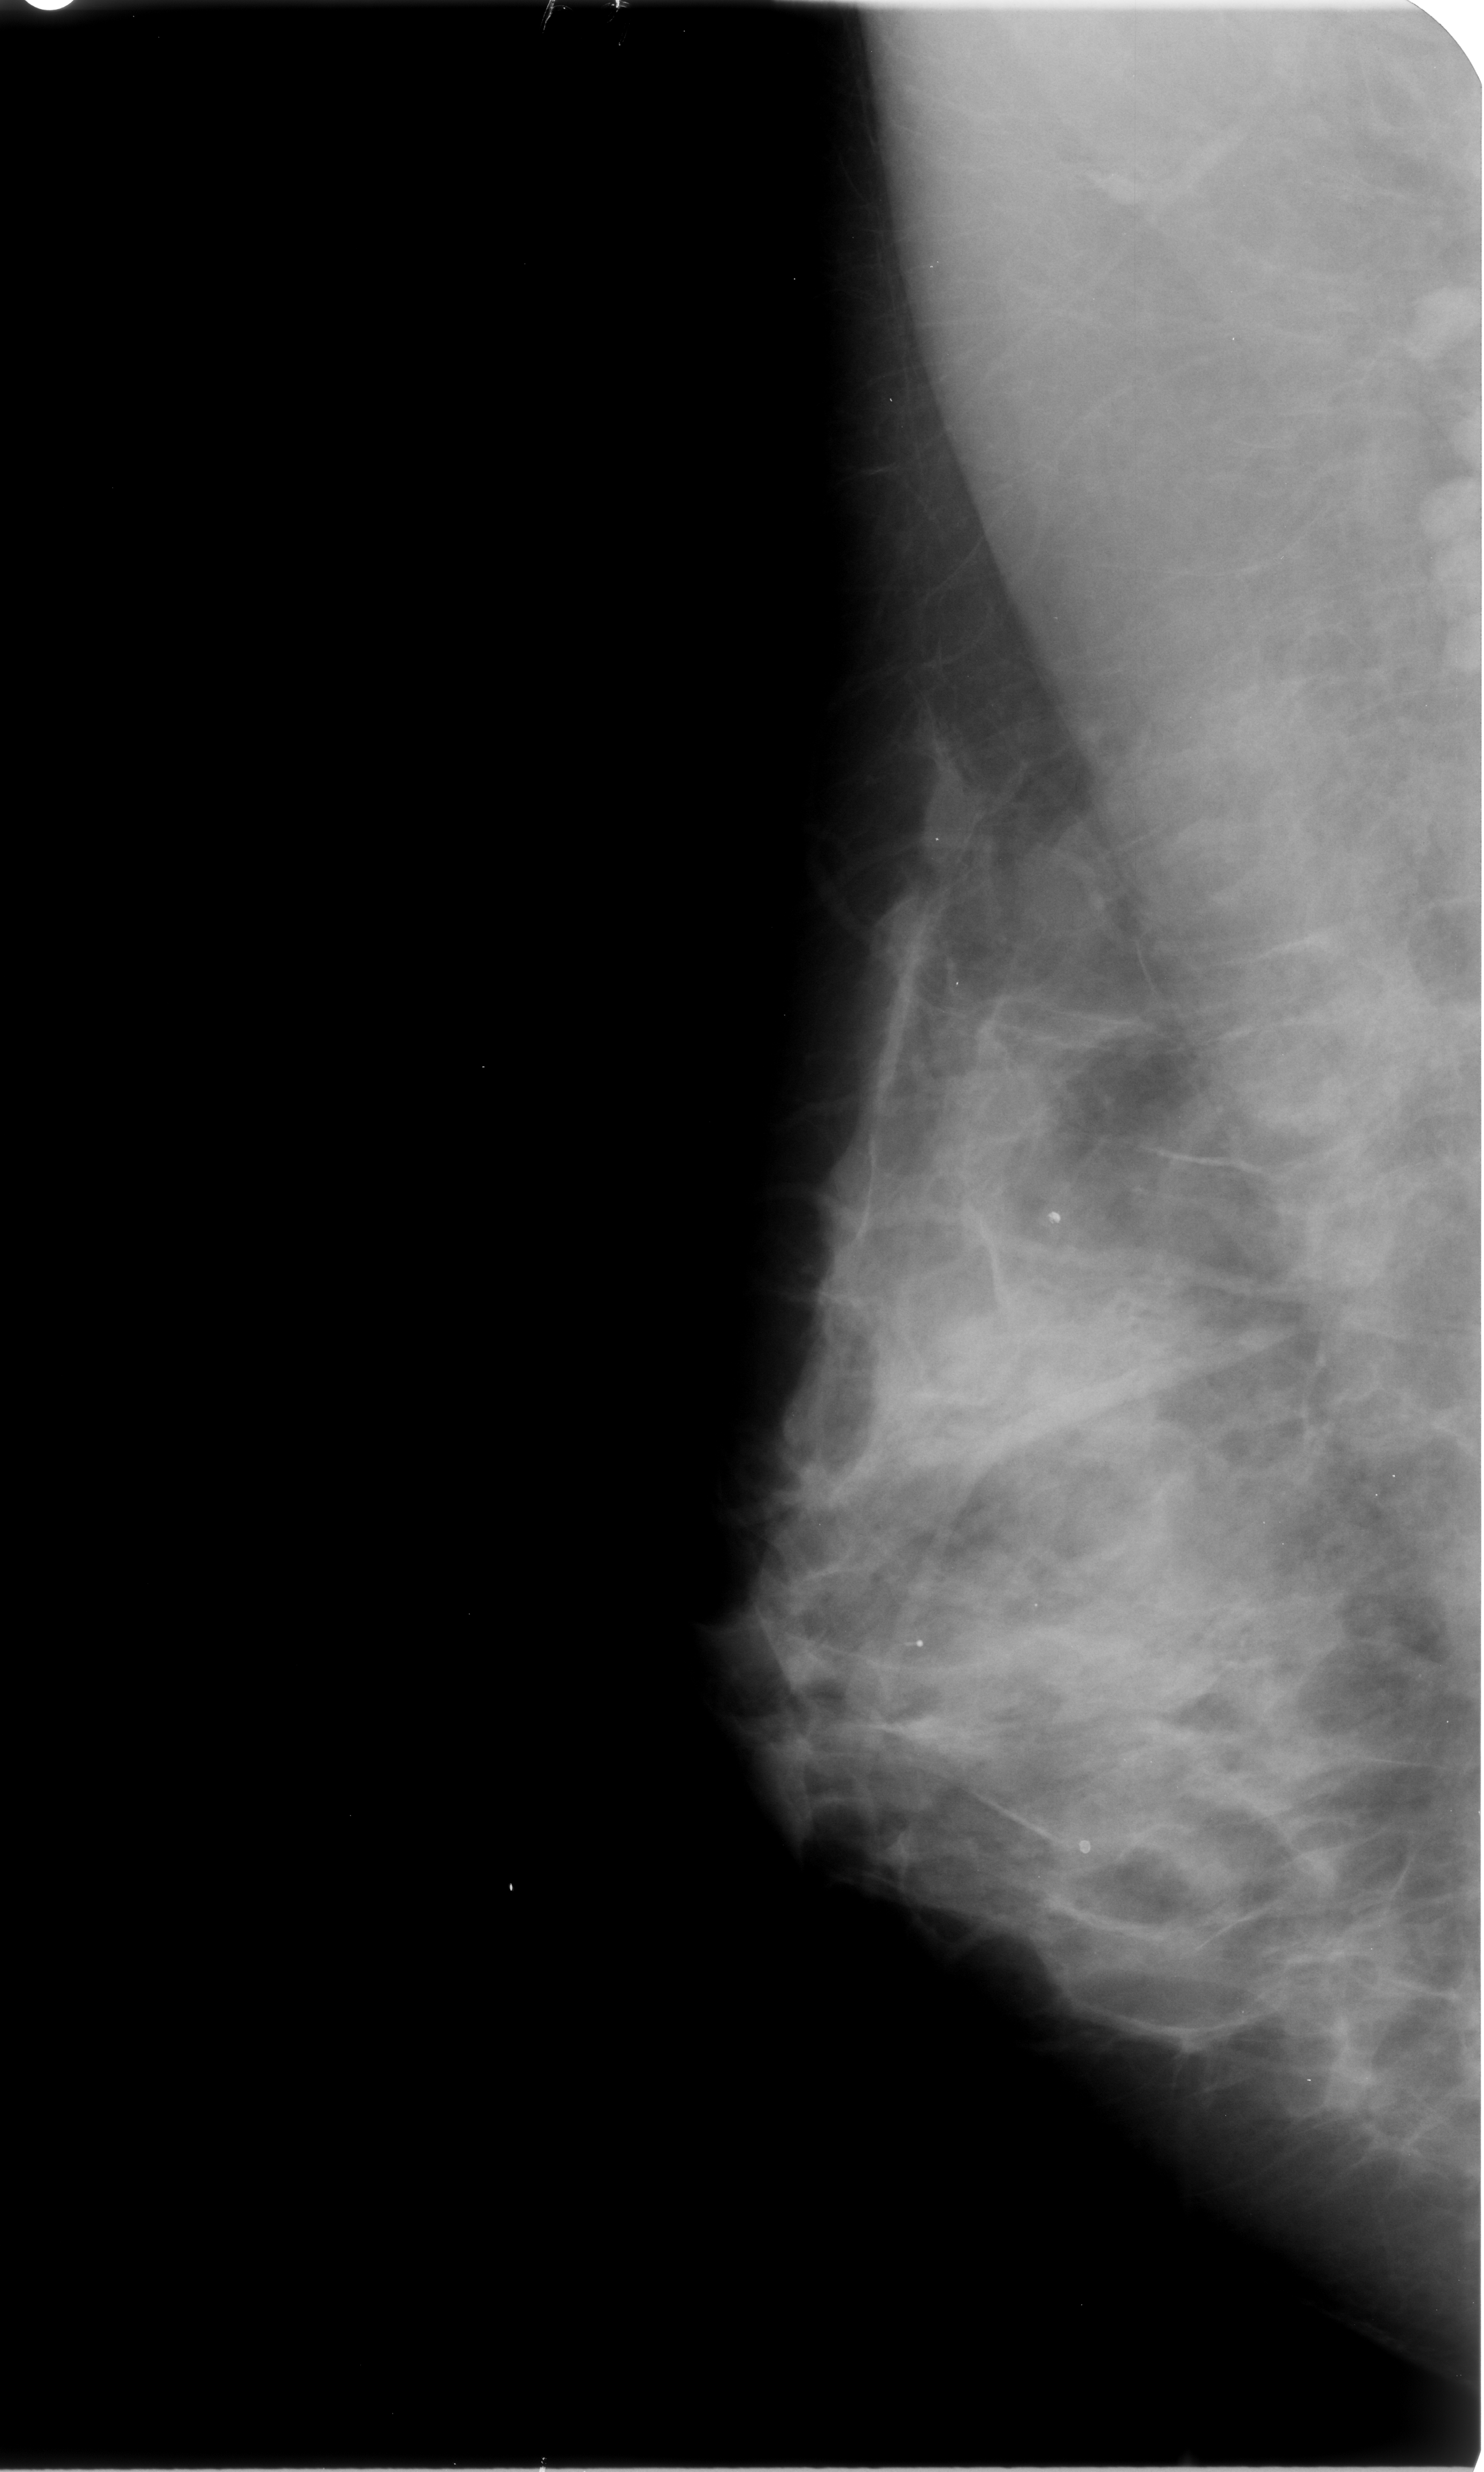
Scanned film-screen mammogram. Right breast. MLO view. Breast composition: heterogeneously dense (BI-RADS density category 3 of 4). 1484 × 2472 image matrix.
Expert-marked regions of interest on this film, with their recorded descriptors:
- Finding 1 of 3: calcifications, morphology round and regular / lucent centered; BI-RADS assessment category 2; benign; no additional work-up was recommended (outcome (as recorded, no biopsy): benign without callback): box from (x=902, y=1620) to (x=933, y=1669) px
- Finding 2 of 3: calcifications, morphology round and regular / lucent centered; BI-RADS assessment category 2; subtlety rating 3 on a 1 (subtle) to 5 (obvious) scale; benign; no additional work-up was recommended (outcome (as recorded, no biopsy): benign without callback): (x=1022, y=1197)–(x=1074, y=1241)
- Finding 3 of 3: calcifications, morphology round and regular / lucent centered; BI-RADS assessment category 2; subtlety rating 3 on a 1 (subtle) to 5 (obvious) scale; outcome (as recorded, no biopsy): benign without callback (not worked up further): (x=1069, y=1826)–(x=1104, y=1866)